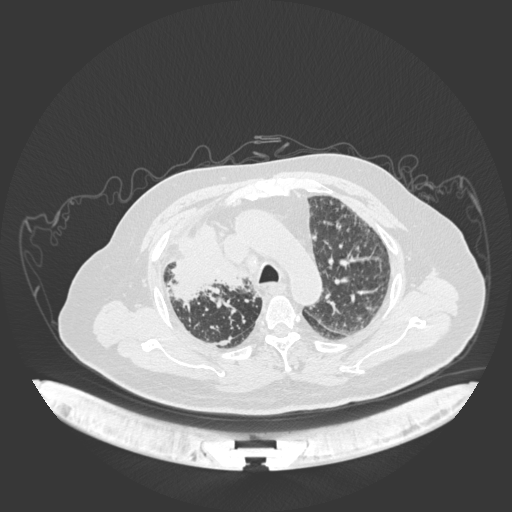
Chest CT, one axial slice; slice 135 of 201 in the series (ordered by position); lung window (W 1500 / L -600 HU); 1 mm slice thickness; 512 × 512 image matrix. Patient: male, 69 years. From the clinical record (not read from this slice): clinical TNM (as recorded): T4 N3 M1.
Structures marked on this image (rectangle marked by the reading radiologist):
- lung tumour (recorded histology: adenocarcinoma): bounding box <165,221,251,304> (left, top, right, bottom; pixels)